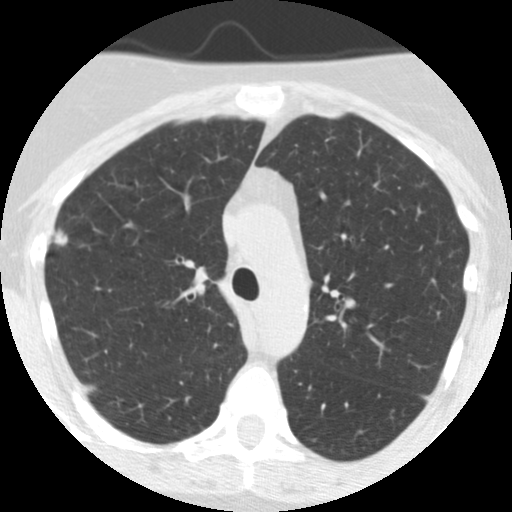
Chest CT (low-dose screening protocol), one axial image, baseline annual screen, lung window (W 1500 / L -600 HU), standard (soft-tissue) reconstruction kernel (STANDARD), slice 172 of 249 in the series, 512 × 512 image matrix. Female, age 55 years at enrolment. Current smoker at enrolment.
- Expert reader's lesion annotation, bounding box [x1, y1, x2, y2] px = [32, 219, 82, 268].
- Reader record for this screening exam (exam-level; its link to the box is not recorded): non-calcified nodule or mass ≥4 mm, right upper lobe, 7 × 7 mm, spiculated (stellate) margins, soft tissue attenuation.
- Official screen result: positive, change unspecified: nodule(s) >= 4 mm or enlarging nodule(s), mass(es), or other non-specific abnormalities suspicious for lung cancer.
- Later outcome: lung cancer diagnosed 1018 days after this screen — bronchiolo-alveolar adenocarcinoma, NOS, right upper lobe, moderately differentiated (G2), stage IIA (AJCC 6th edition), 13 mm at pathology.